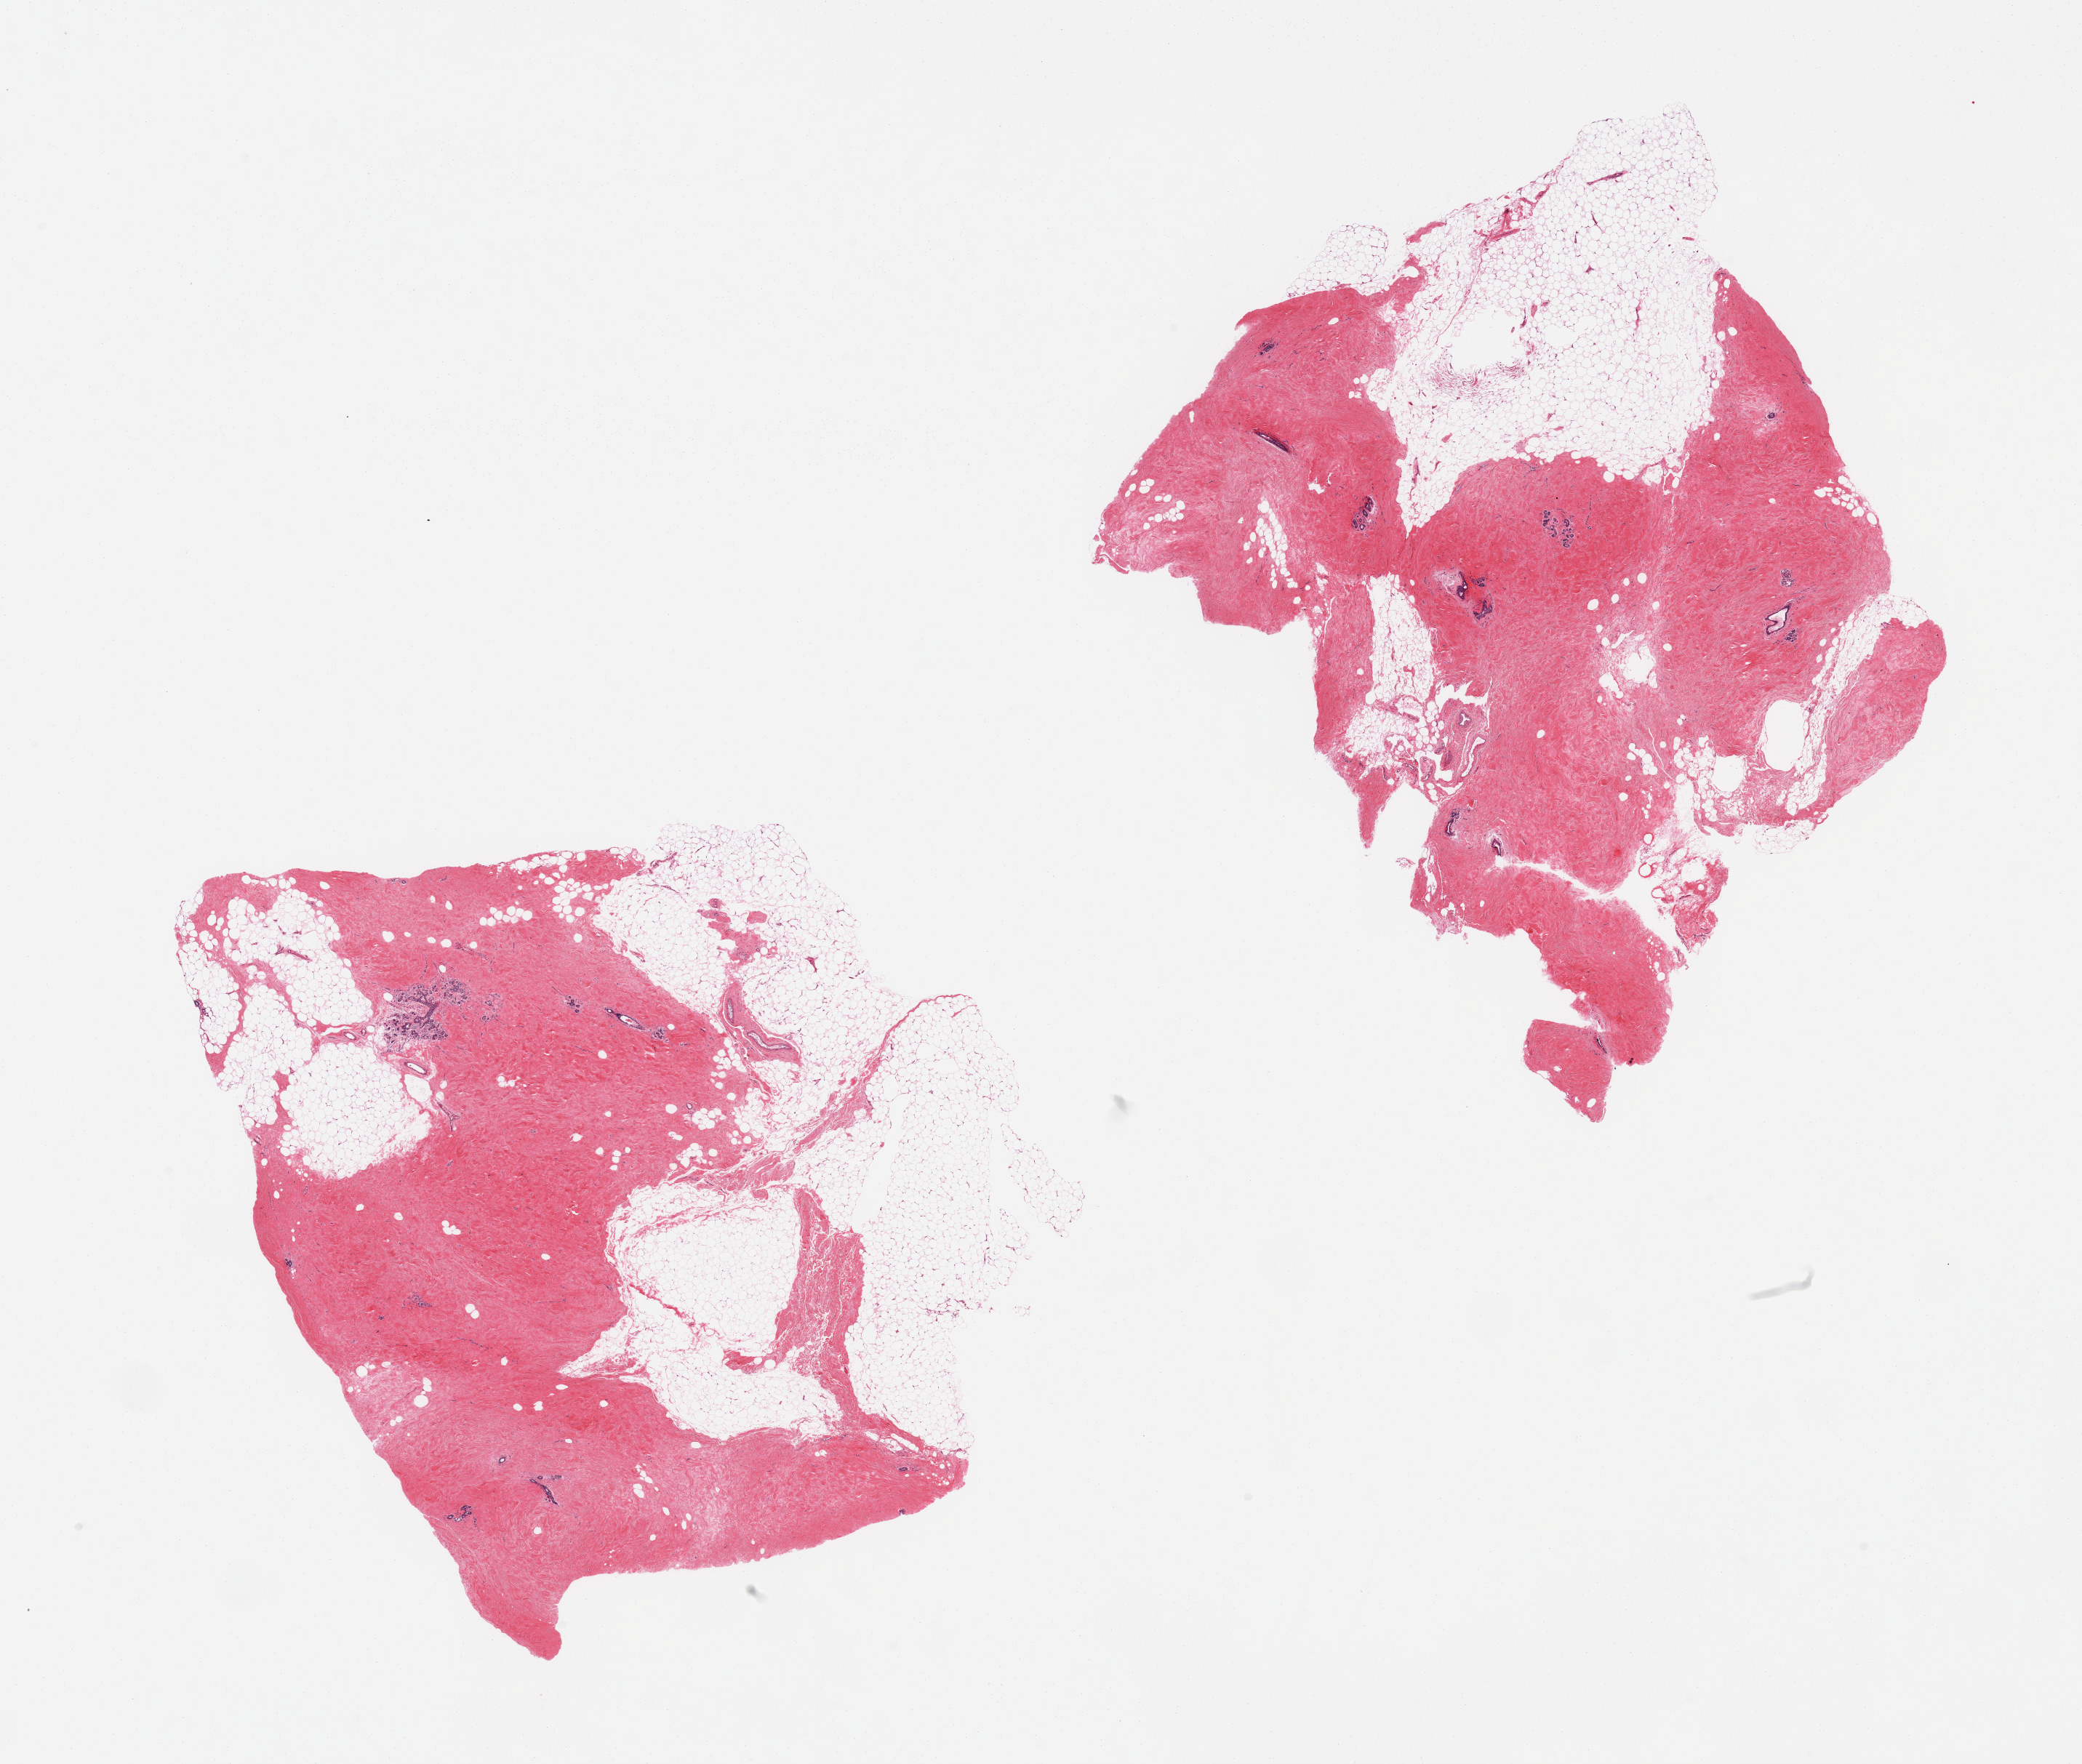
H&E whole-slide image — low-resolution overview of the scanned area, about 22.6 x 19.2 mm, PAXgene-fixed paraffin-embedded (PFPE) section, section of breast (target tissue), donor tissue sample. Female donor.
Pathologist's review note for this sample: 2 pieces, fibrous mastopathy; ductal-lobular units.